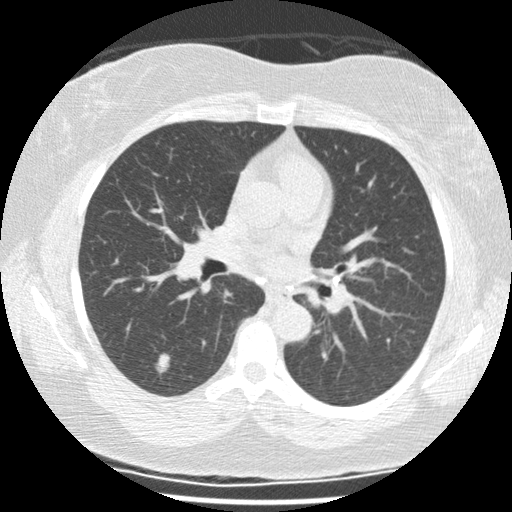
Low-dose screening chest CT, one axial slice; slice 64 of 117 in the series (ordered by position); 120 kVp; lung window (W 1500 / L -600 HU); 2.5 mm slice thickness; 512 × 512 image matrix, field of view 325 × 325 mm.
Structures marked on this image (outlined manually by an expert reader):
- lesion 1 (tumor, lower lobe of right lung): bounding box <155,353,170,374> (left, top, right, bottom; pixels)